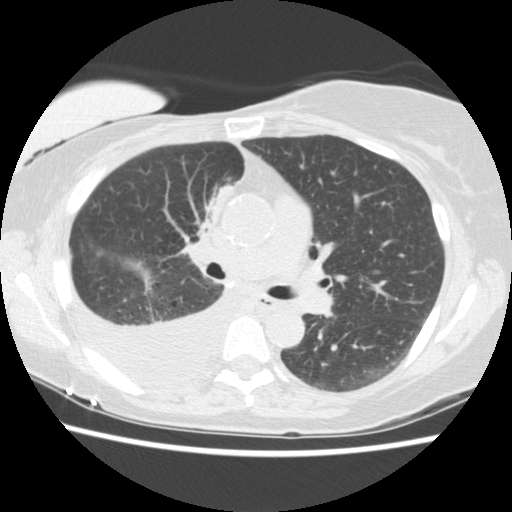
Low-dose screening chest CT, one axial slice. Lung window (W 1500 / L -600 HU). 2.5 mm slice thickness. 512 × 512 image matrix.
Outlined on this slice (expert manual segmentation):
- lesion 1 (tumor, upper lobe of right lung): bounding box <208,184,233,223> (left, top, right, bottom; pixels)